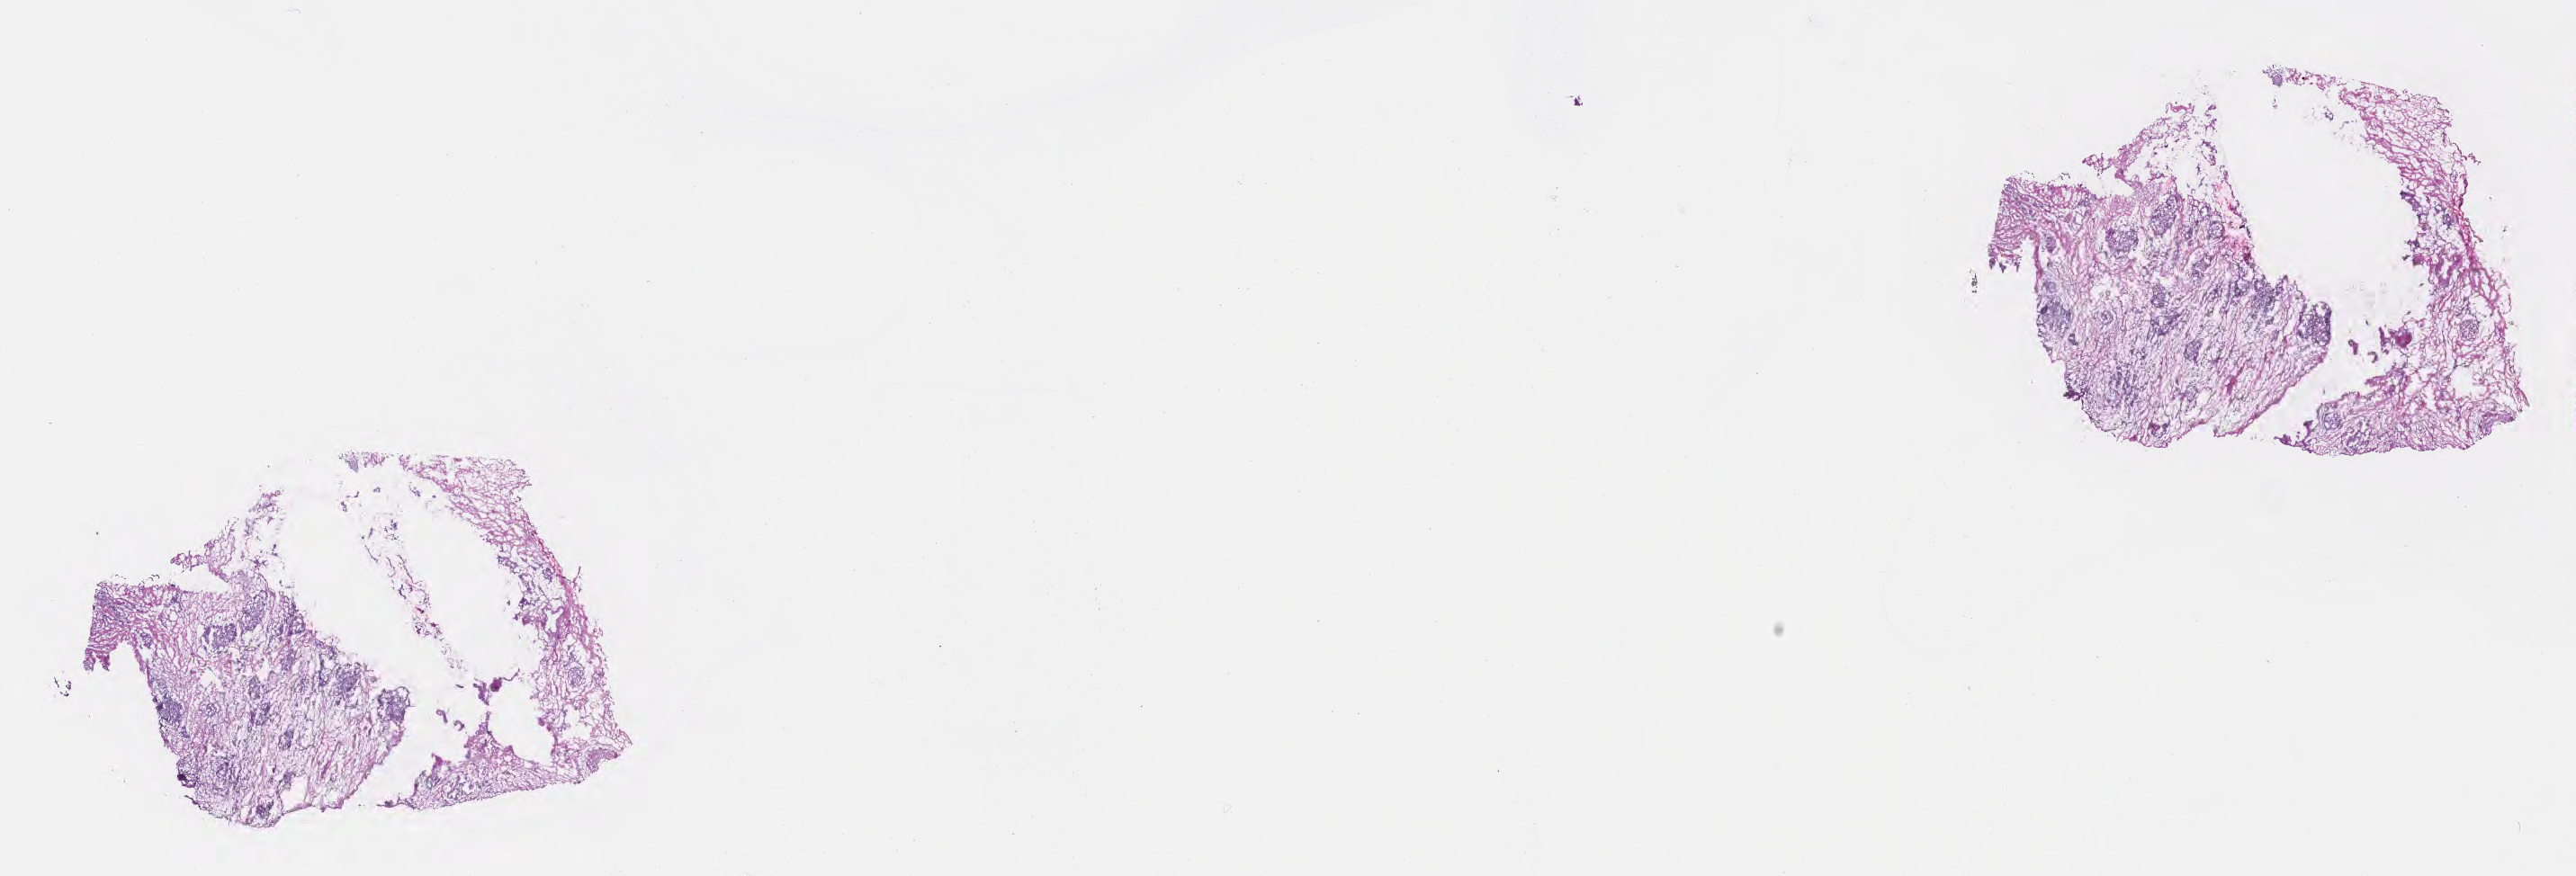
Haematoxylin and eosin whole-slide image — low-resolution overview of the scanned area, about 23.1 x 7.9 mm; cryosection; specimen: primary tumor; anatomic site: body of pancreas. Patient: female, age at initial diagnosis 64 years. Pathologist review of this section (percent, as recorded): tumor cells 100%, tumor nuclei 40%, stromal cells 0%, necrosis 0%, normal cells 0%. Inflammatory infiltration, as recorded: lymphocyte infiltration 0%, monocyte infiltration 0%, neutrophil infiltration 0%.
• section: bottom of the tissue portion
• diagnosis: Adenocarcinoma, NOS
• AJCC pathologic stage: Stage IIB